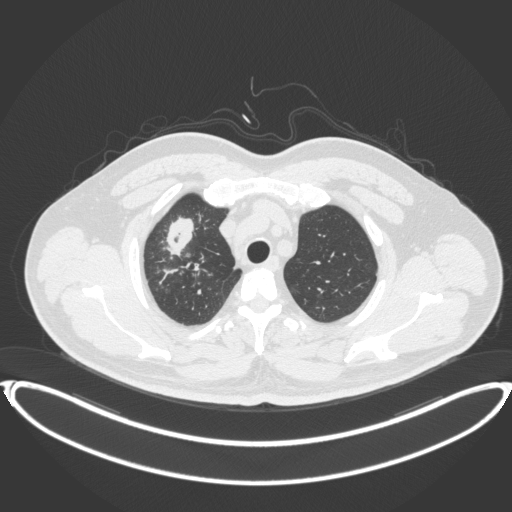
Chest CT, one axial slice. Position 323 of 399 along the scan axis. Reconstruction kernel B31f. 120 kVp. Lung window (W 1500 / L -600 HU). 1 mm slice thickness. 512 × 512 image matrix, field of view 445 × 445 mm. Male patient, age 53 years. From the clinical record (not read from this slice): clinical TNM (as recorded): T2a N0 M0.
Annotated regions visible in this slice (rectangle marked by the reading radiologist):
- lung tumour (recorded histology: adenocarcinoma): bounding box <158,213,196,257> (left, top, right, bottom; pixels)